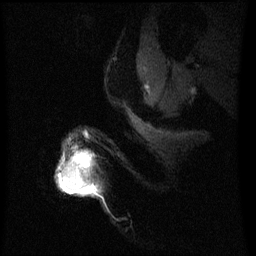
Breast MRI (dynamic contrast-enhanced), one sagittal slice. Slice 50 of 60 in the series (ordered by position). Dynamic contrast-enhanced series, image 2 of 3 at this slice position (ordered by acquisition). 1.5 T. TE 4.2 ms, TR 8 ms. 2.2 mm slice thickness. 256 × 256 image matrix, field of view 200 × 200 mm. Patient: female, 50 years.
Outlined on this slice (semi-automatic segmentation, software-assisted and operator-edited):
- analysis volume of interest (the breast-tissue region the enhancement analysis was run in; not a lesion): bounding box [x1, y1, x2, y2] px = [62, 156, 88, 193]
- tumour enhancement mask (voxels above the 70 % enhancement threshold inside the analysis volume of interest): [62, 156, 88, 193]